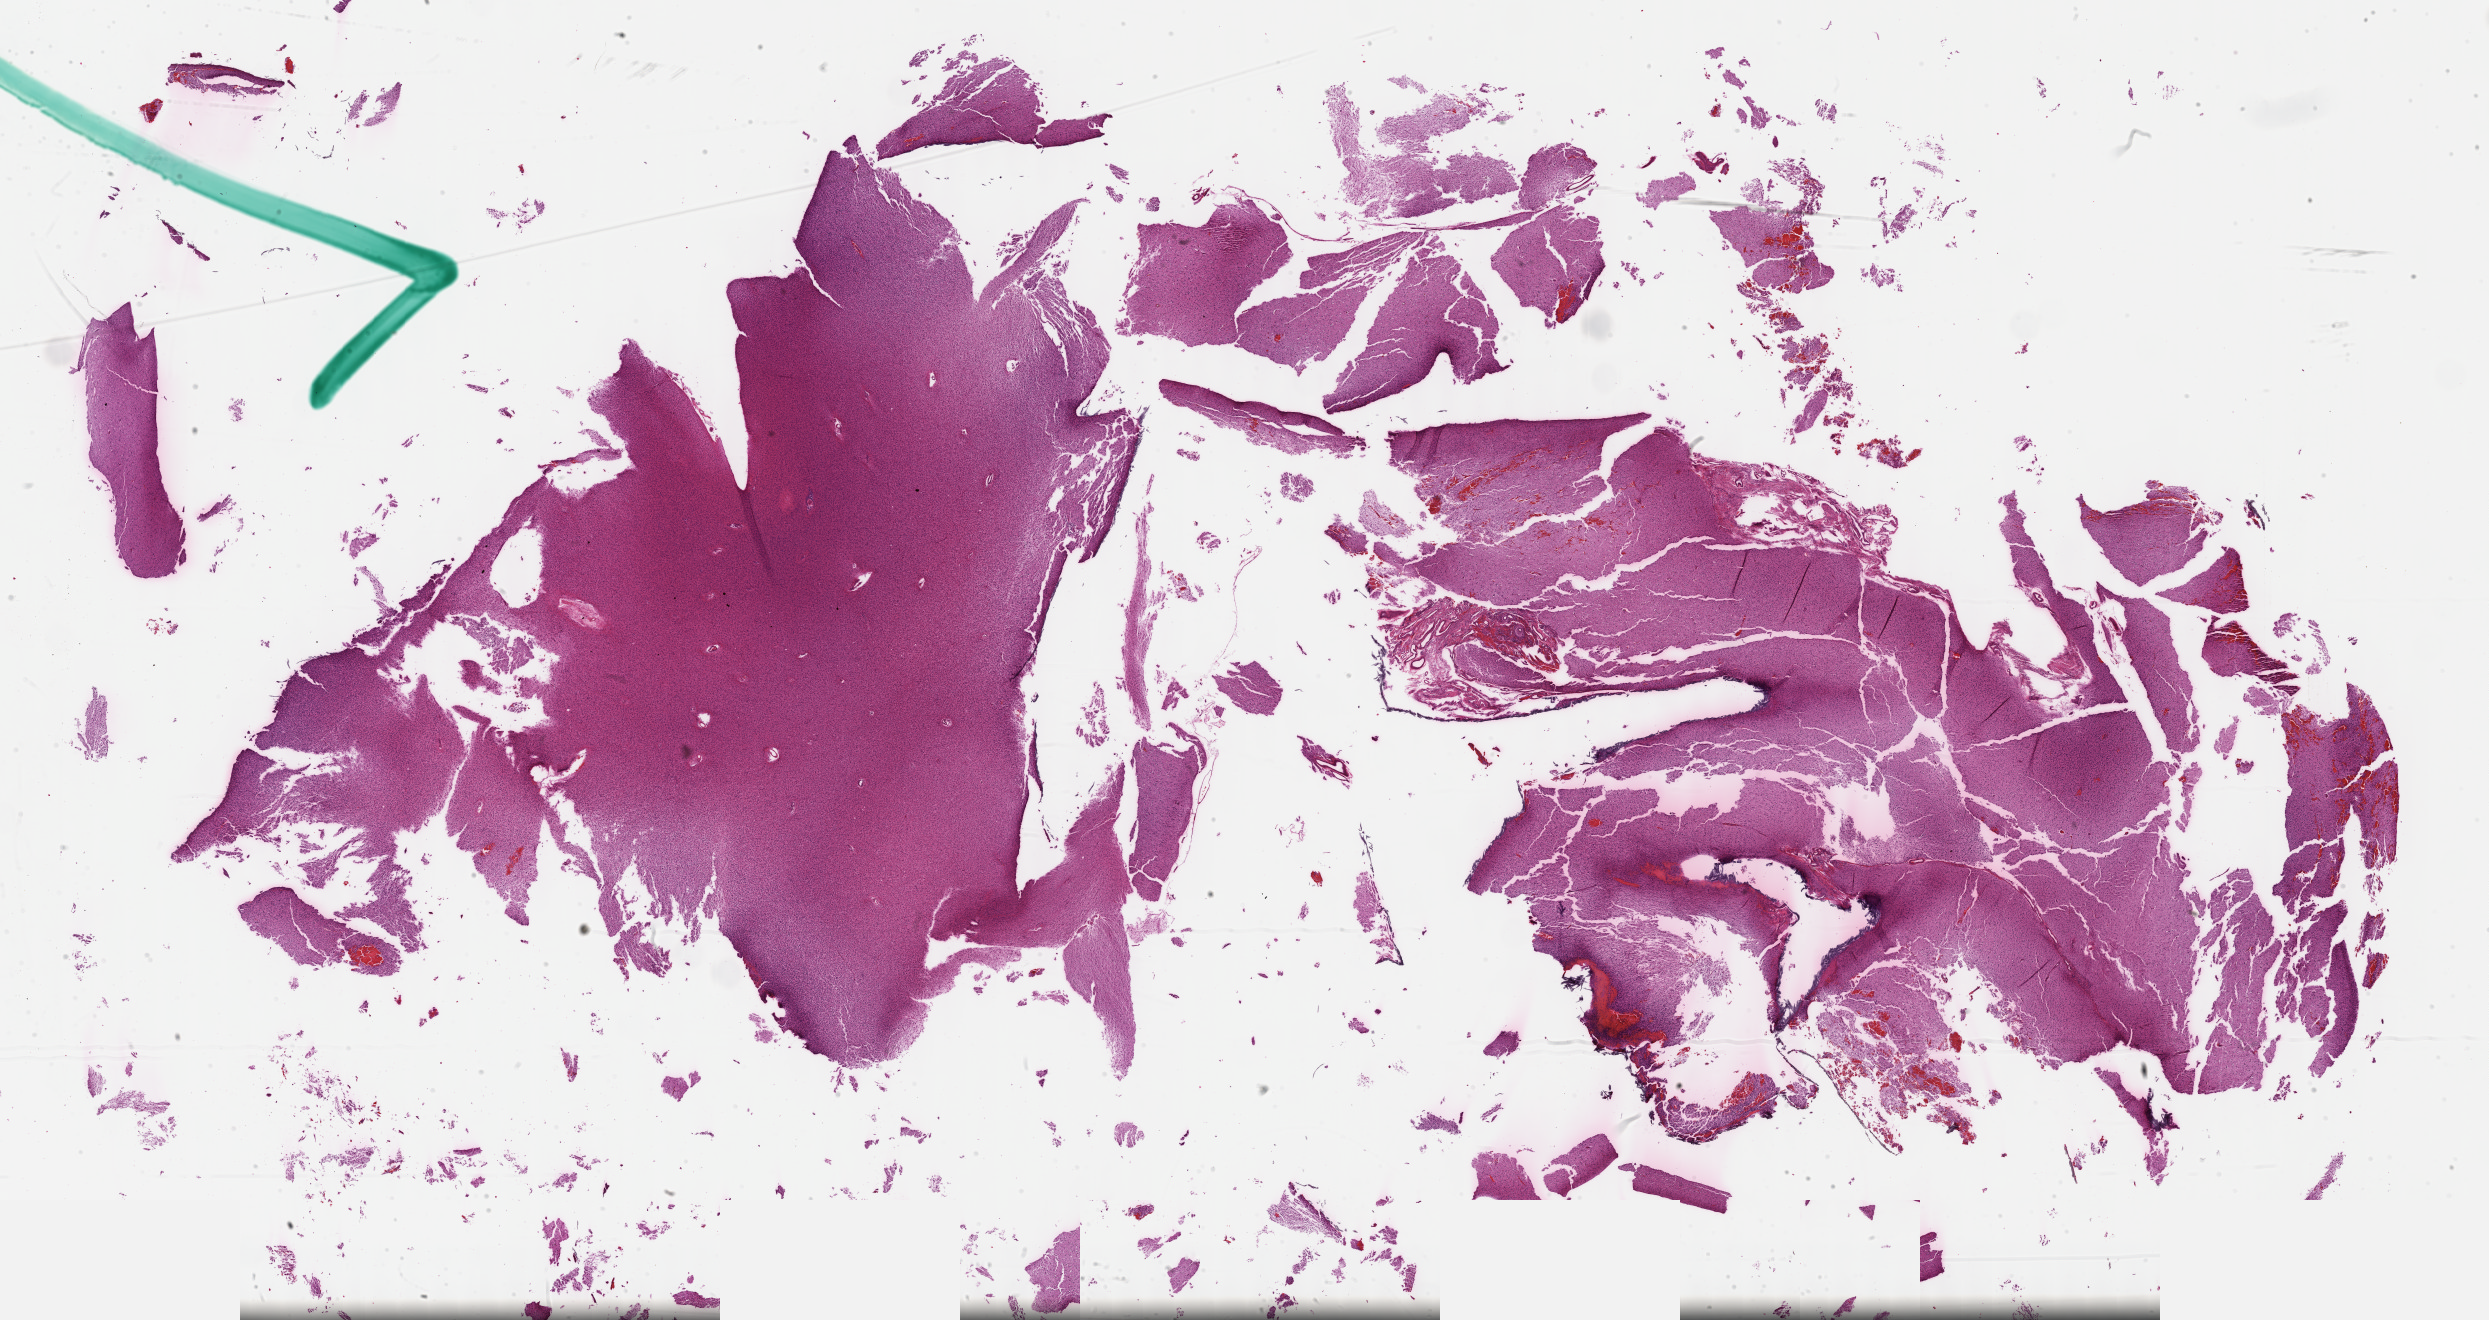
H&E whole-slide image, a low-resolution overview of the entire scanned area, about 40.3 x 21.4 mm. Formalin-fixed paraffin-embedded (FFPE) diagnostic section. Brain, primary tumour sample. Patient: female, age at initial diagnosis 34 years. Histologic grade: G2 (moderately differentiated).
Diagnosis: Astrocytoma, NOS (cerebrum).